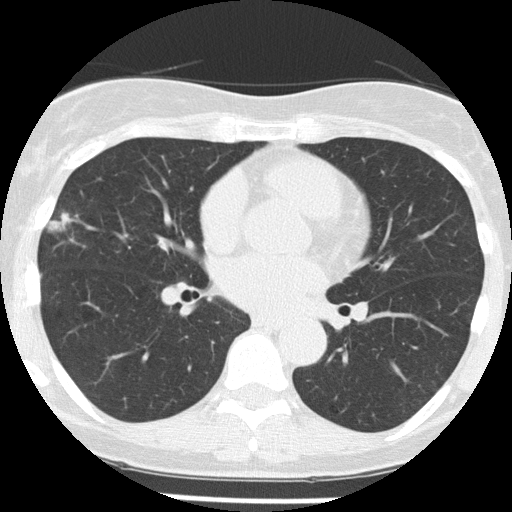
Low-dose screening chest CT, one axial slice; position 81 of 156 along the scan axis; reconstruction kernel FC51; 120 kVp; lung window (W 1500 / L -600 HU); 512 × 512 image matrix, field of view 280 × 280 mm.
Structures marked on this image (manually delineated by an expert):
- lesion 1 (tumor, middle lobe of right lung): bounding box [x1, y1, x2, y2] px = [46, 212, 72, 232]